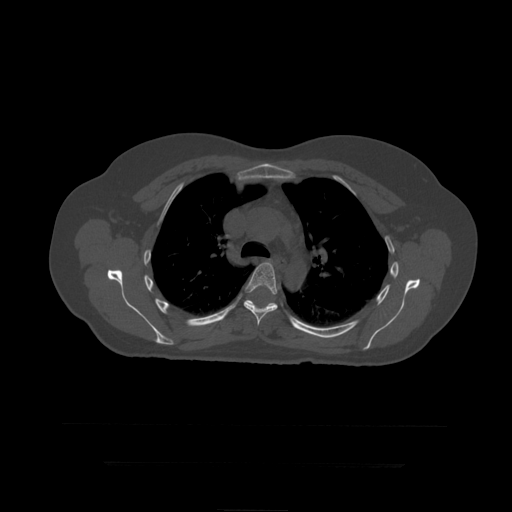
CT including the spine, one axial slice; bone window (W 1800 / L 400 HU); 1.25 mm slice thickness; 512 × 512 image matrix. Patient age 41 years. From the clinical record (not read from this slice): primary cancer: breast.
Structures marked on this image (semi-automatic segmentation, software-assisted and operator-edited):
- T6 vertebra: bounding box [x1, y1, x2, y2] px = [244, 262, 278, 326]
- T7 vertebra: [247, 300, 275, 305]